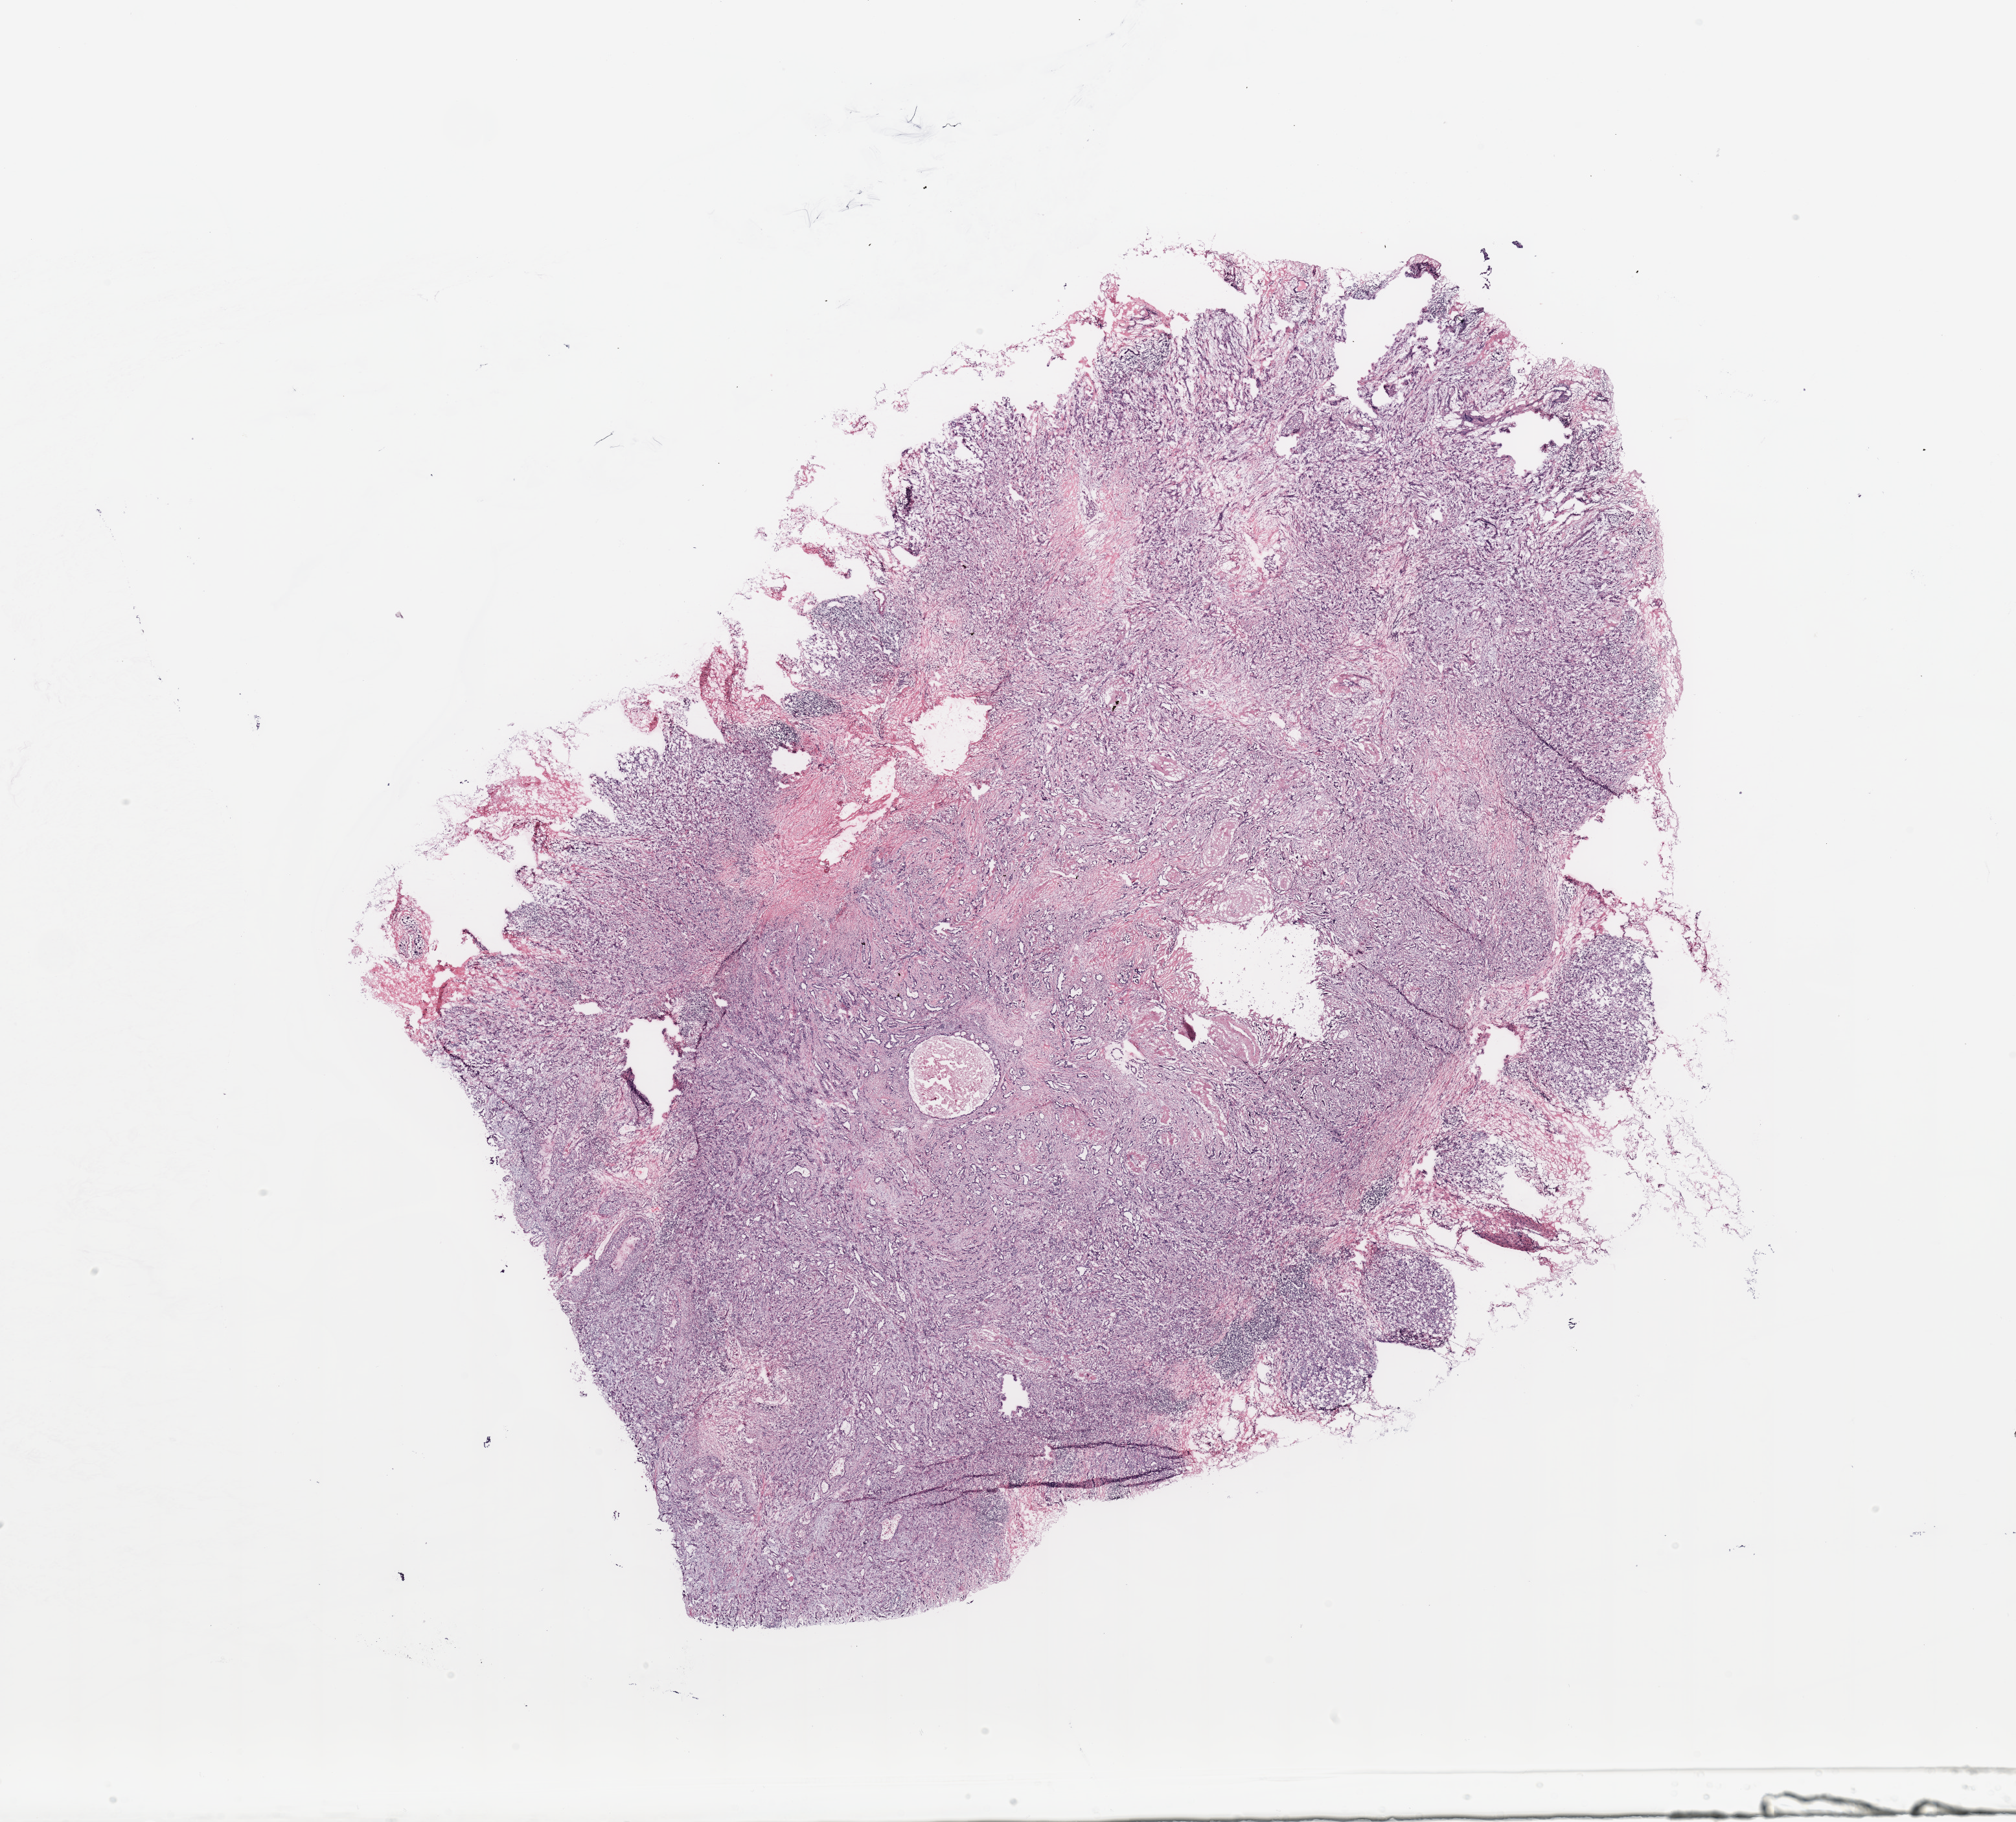
Whole-slide histology image, H&E — low-resolution overview of the scanned area, about 24.6 x 22.2 mm (slide scanned at 20x), breast, tissue type not recorded.
Patient diagnosis (cohort enrolment): breast cancer (breast).